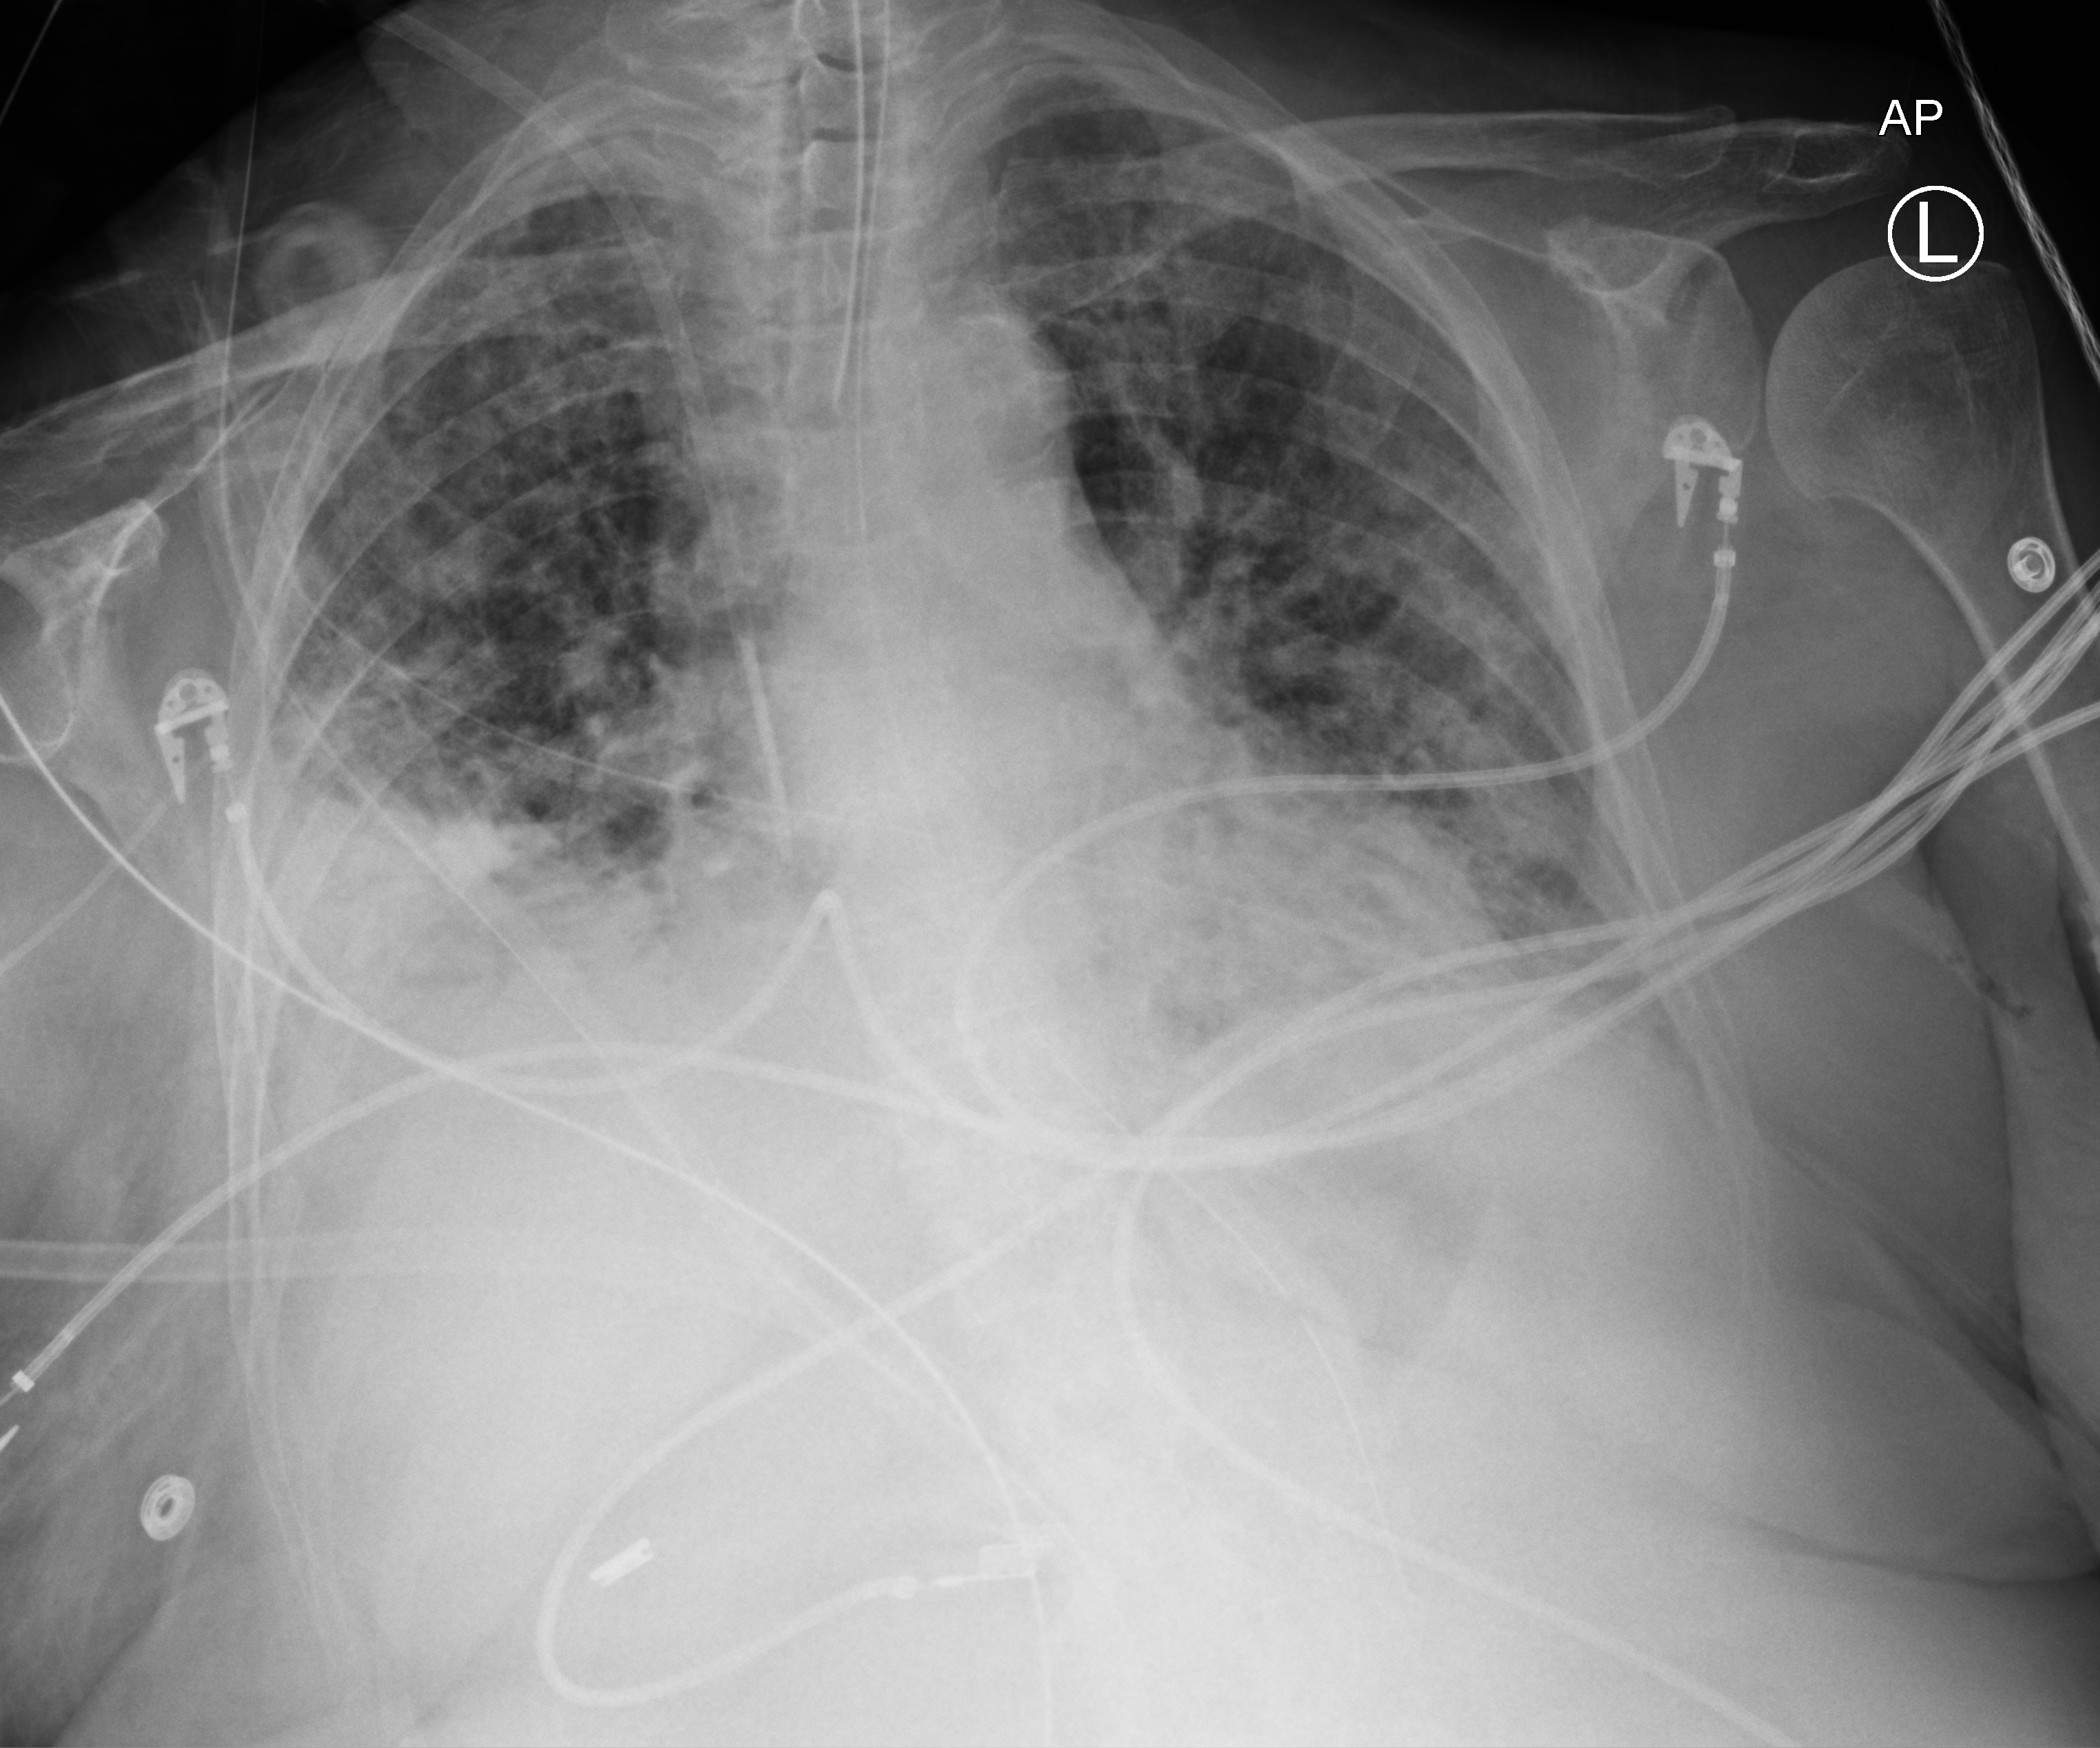
Bedside chest radiograph (computed radiography); anteroposterior (AP) projection. Female patient hospitalised with COVID-19, age 75–90 years.
From the hospital-stay record, not from the radiograph (when in the stay this image was taken is not recorded): admitted to intensive care during this hospital stay: yes; other chronic lung disease (admission record): no; smoking status (admission record): former.